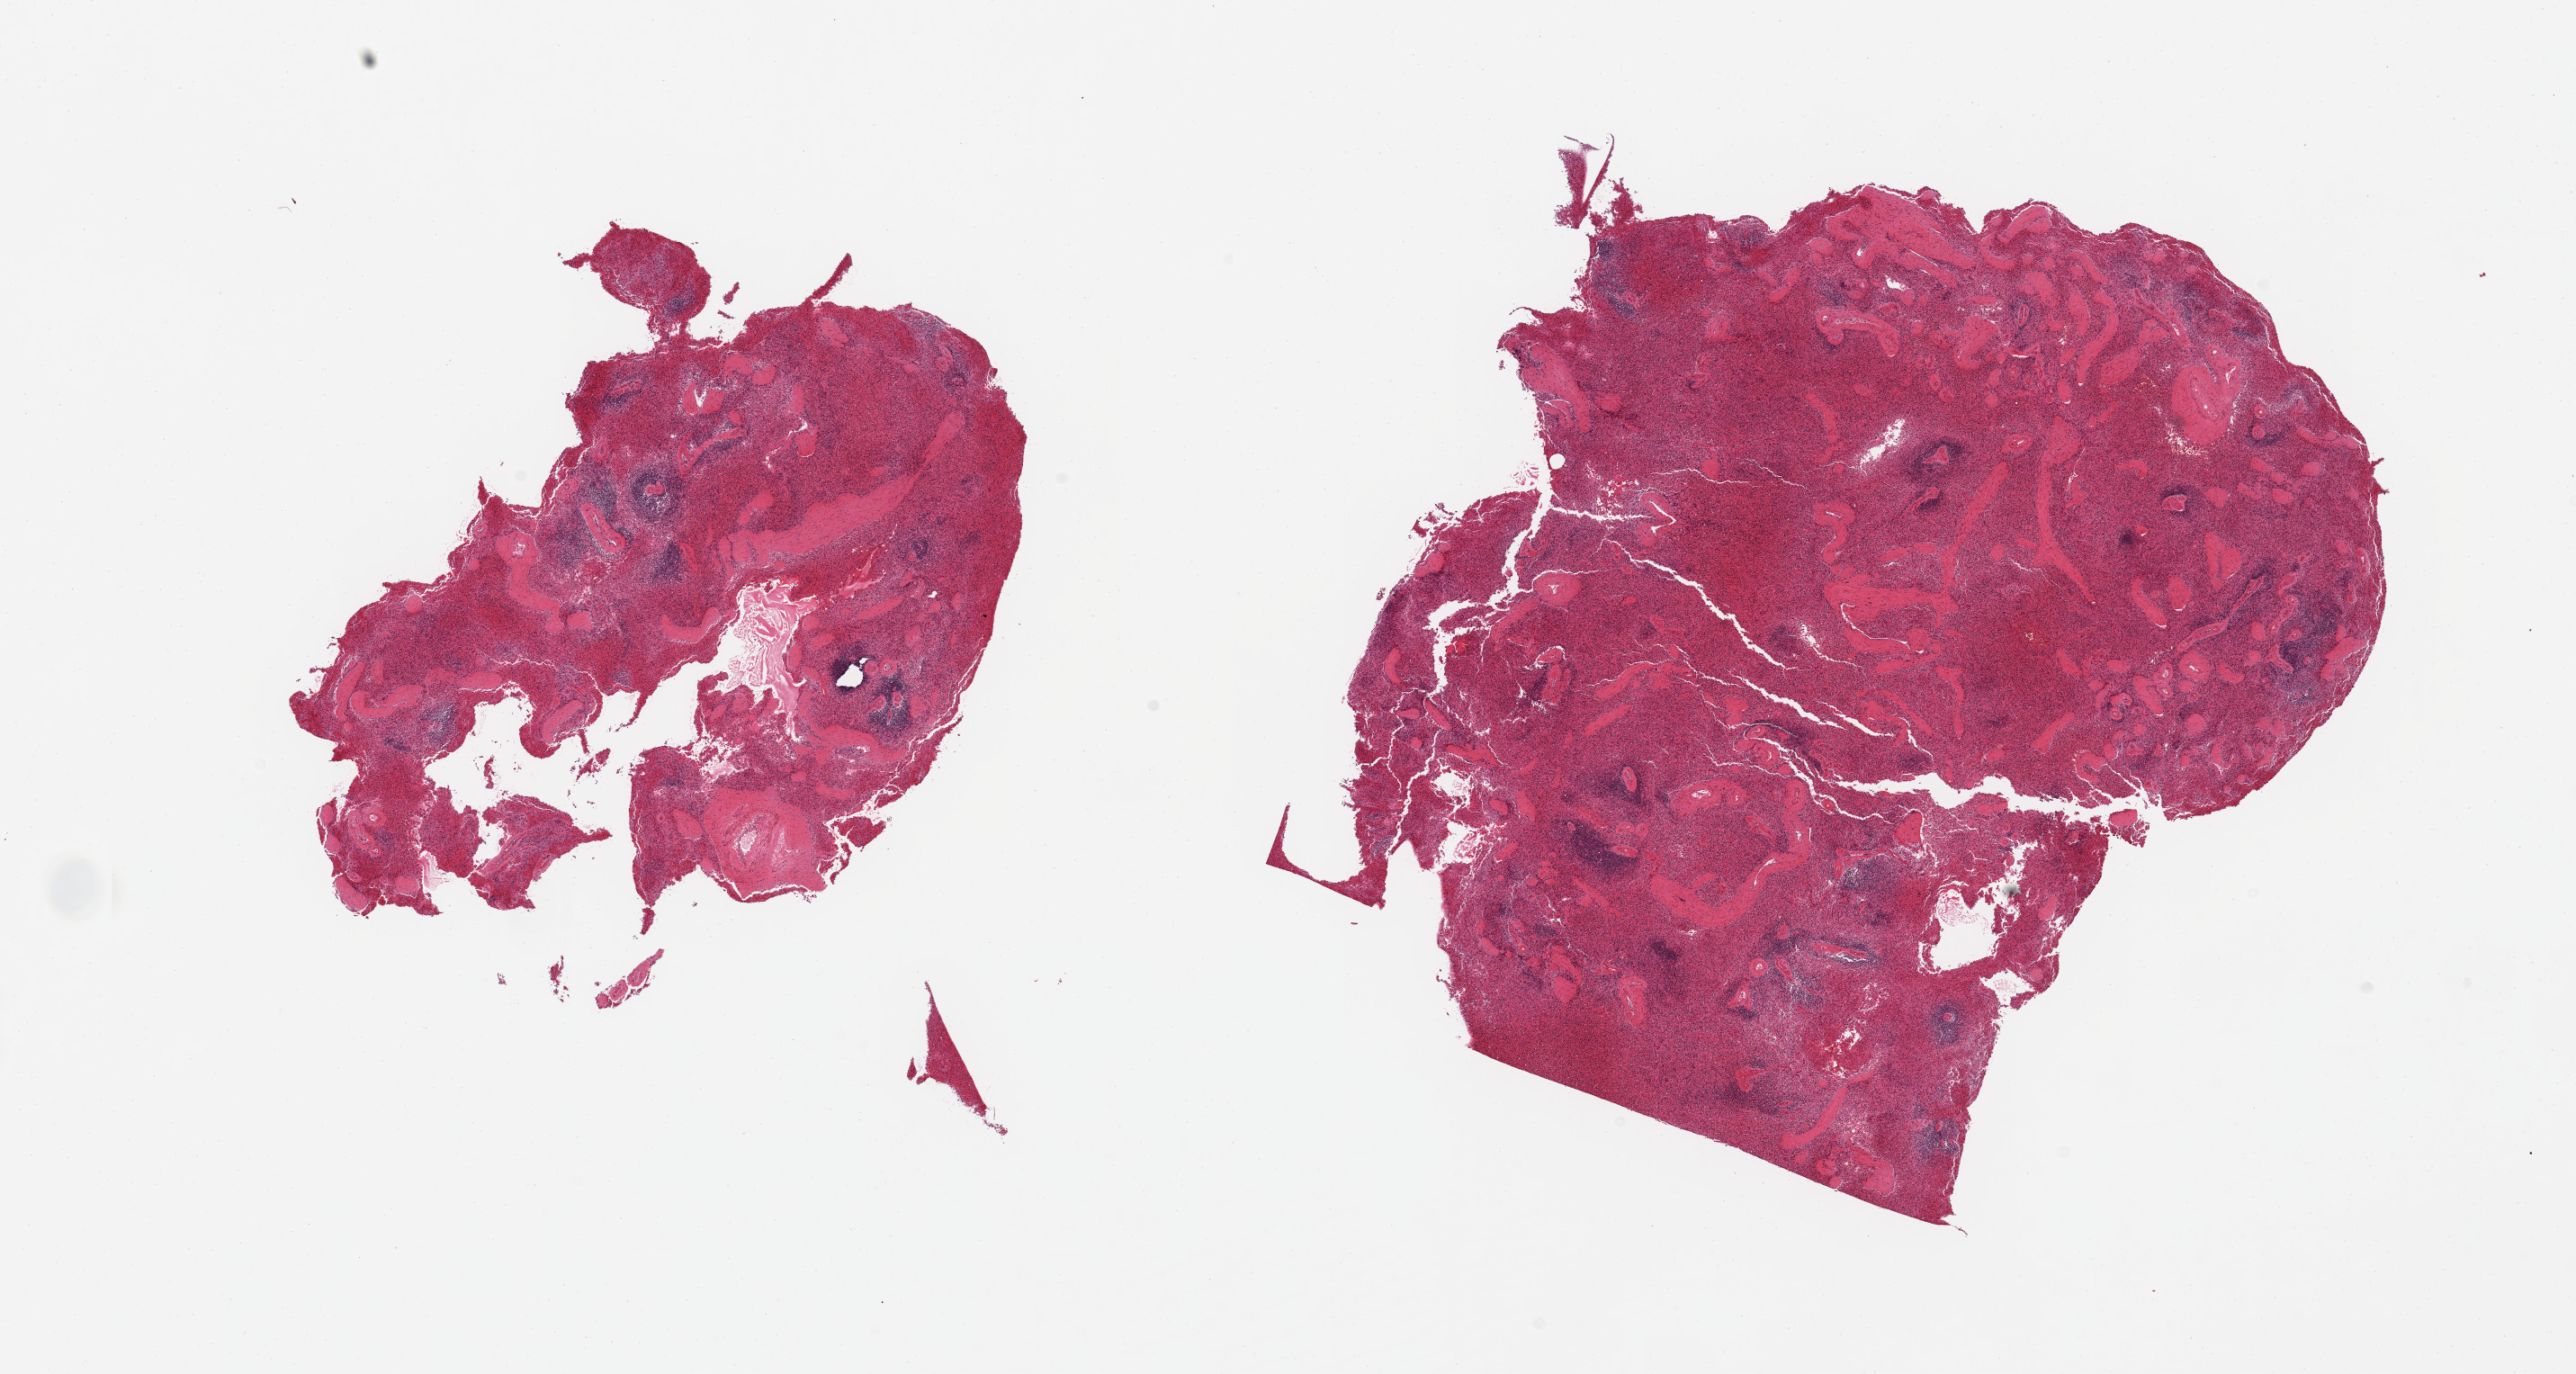
Hematoxylin and eosin (H&E) whole-slide image, brightfield — a low-resolution overview of the entire scanned area, about 22.6 x 12.1 mm (slide scanned at 20x). PAXgene-fixed paraffin-embedded (PFPE) section. Sampled site (target tissue): spleen. Donor tissue sample.
Review note (as recorded): 2 pieces; moderate congestion and fragmention.